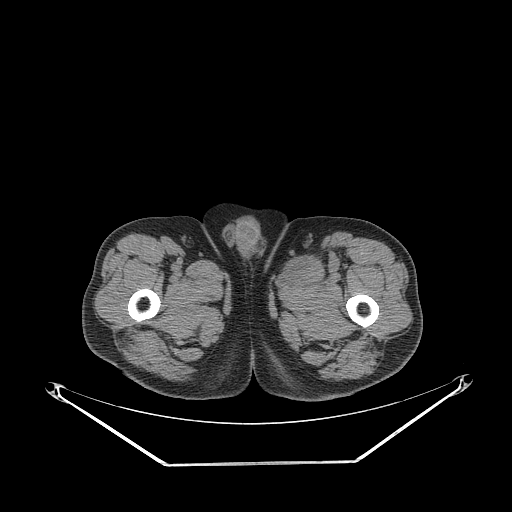
CT of an extremity soft-tissue mass (from a PET/CT study), one axial slice. Reconstruction kernel STANDARD. Soft-tissue window (W 400 / L 40 HU). 3.75 mm slice thickness. 512 × 512 image matrix, field of view 500 × 500 mm. Male patient. Case-level facts recorded for this patient, not image findings: histological type: pleiomorphic liposarcoma; grade: high; site of the primary tumour: left thigh.
Outlined on this slice (expert contour drawn on MRI and transferred to this co-registered scan by the dataset authors):
- gross tumour volume including surrounding oedema: bounding box [x1, y1, x2, y2] px = [283, 247, 344, 282]
- gross tumour volume (mass): [283, 254, 318, 280]